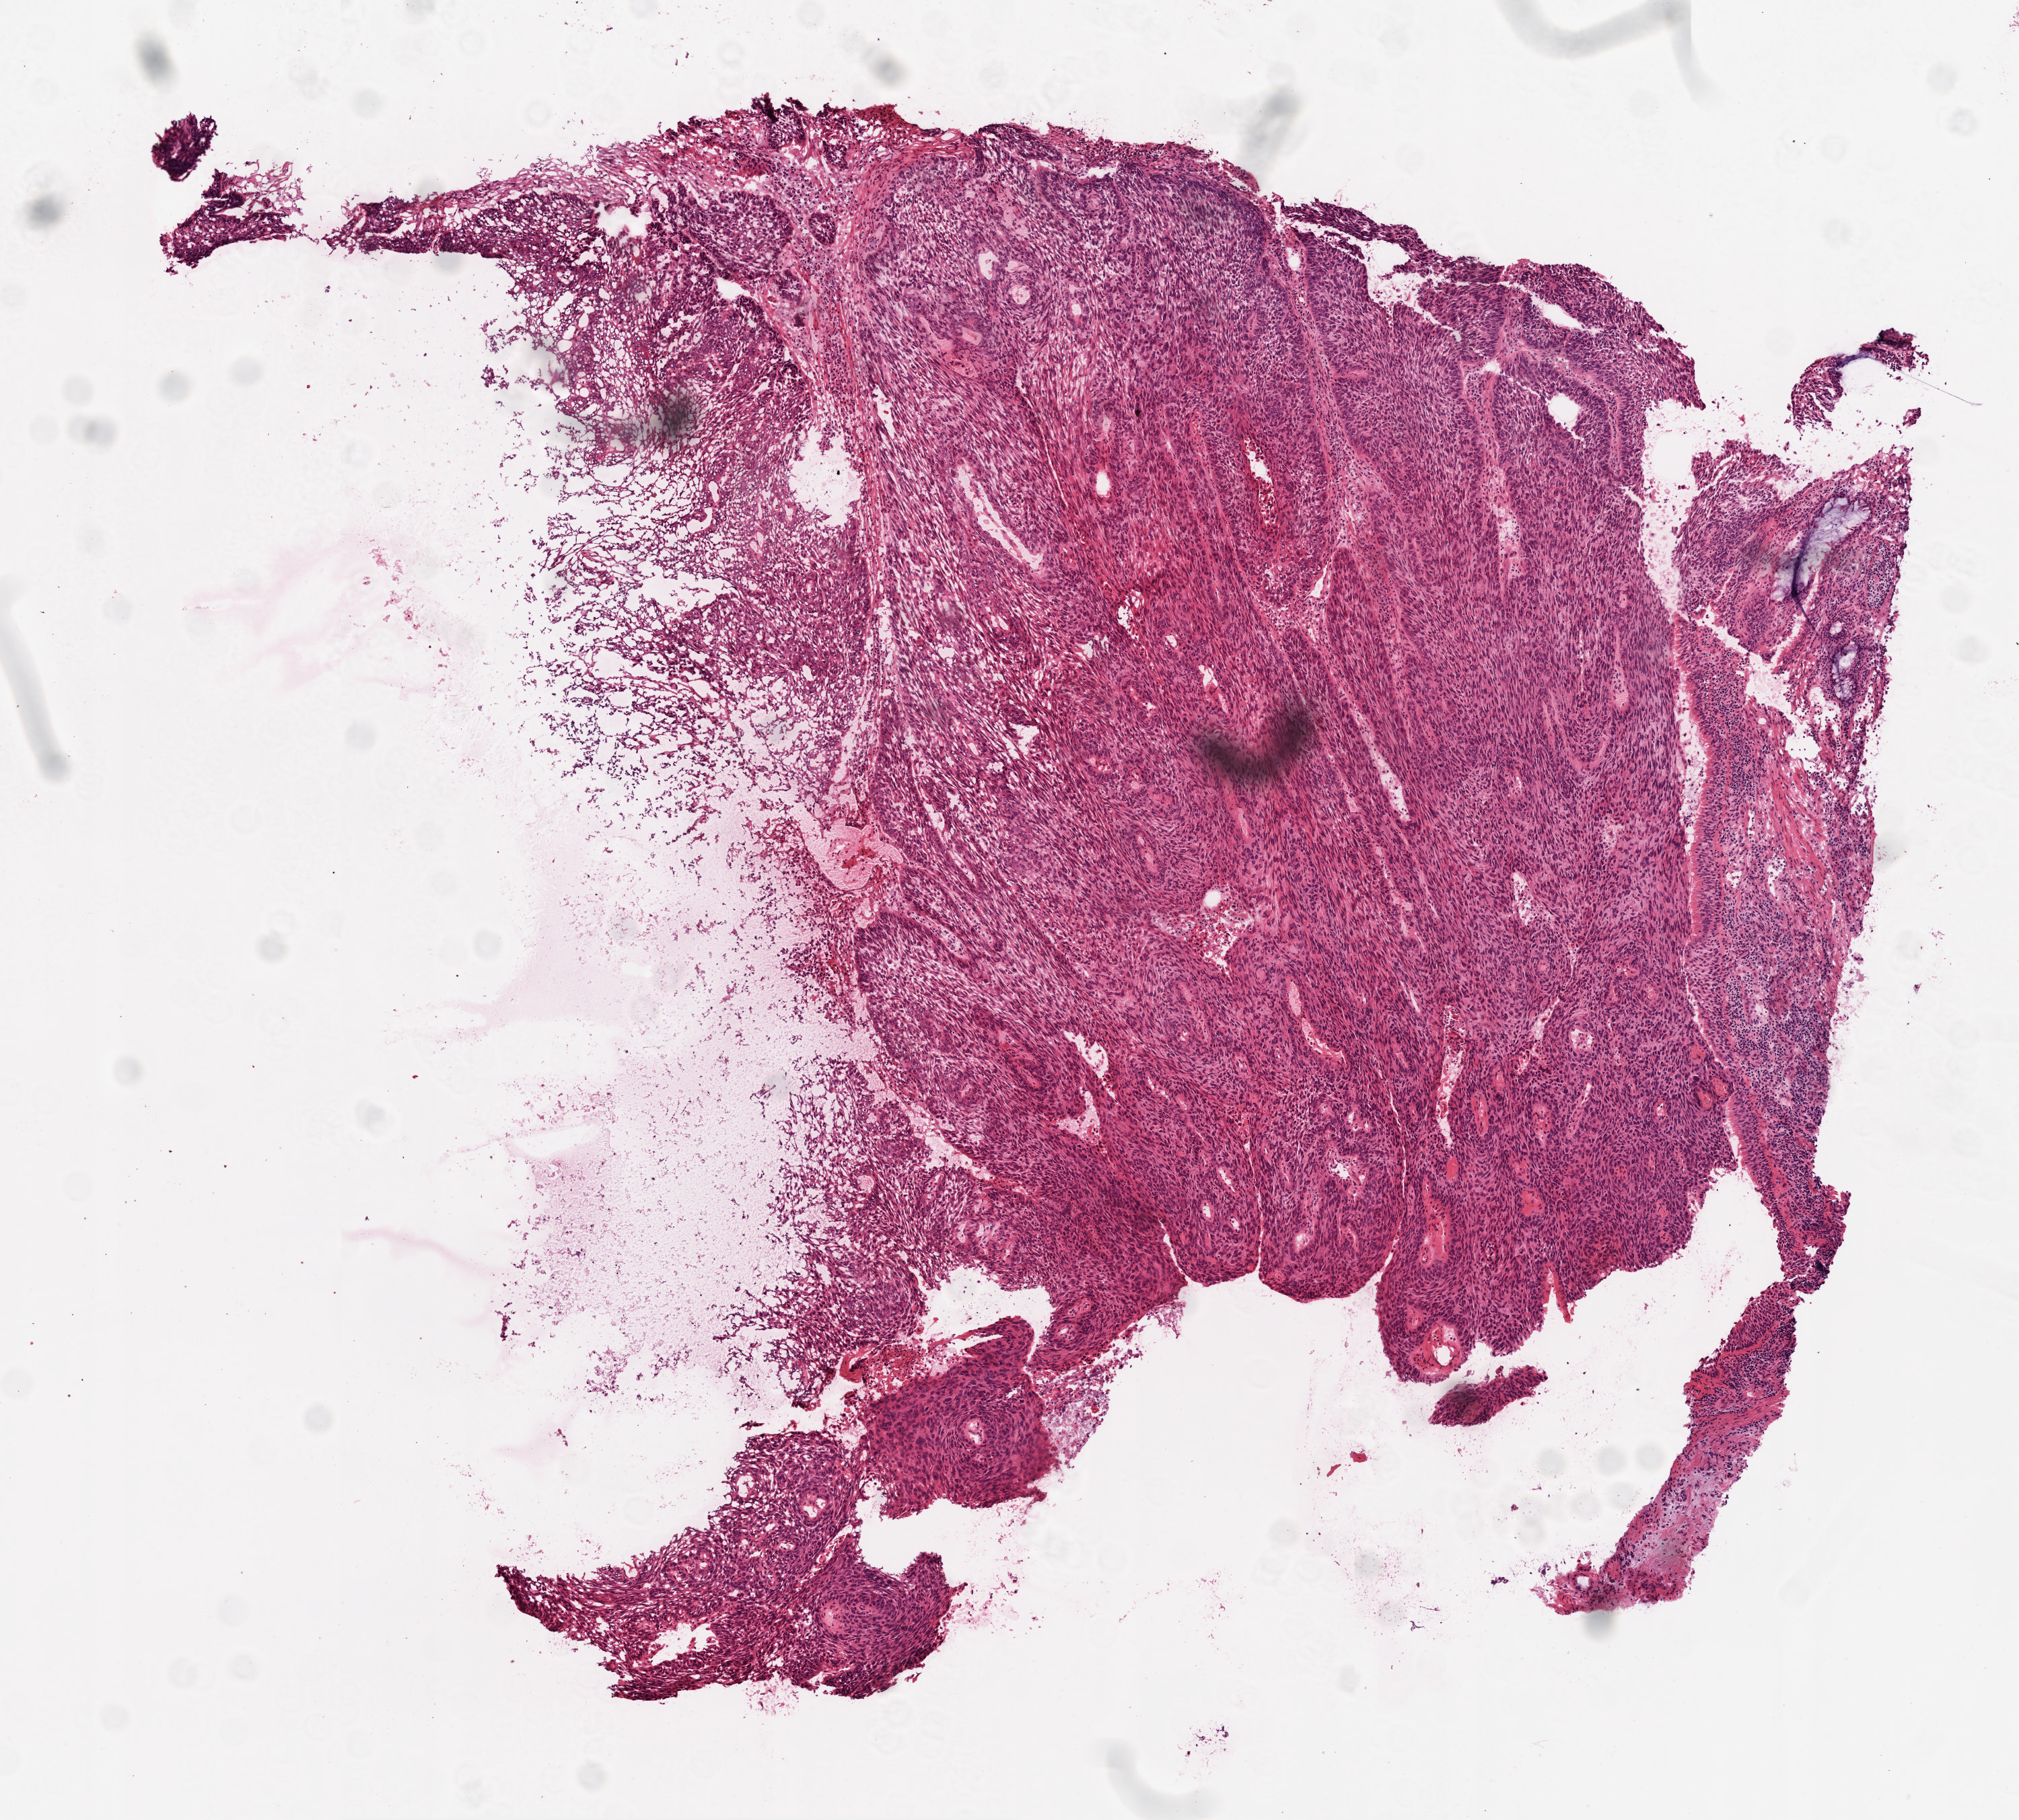
Digitized H&E tissue section (whole slide) — whole scanned area (about 6.0 x 5.4 mm, slide scanned at 20x) shown as a low-resolution overview. Frozen section from the top of the tissue portion. Lung, primary tumour sample. Male patient; age at initial diagnosis 66 years. Slide review estimates, as recorded: tumour cells 75%, tumour nuclei 70%, normal cells 15%, stromal cells 10%, necrosis 0%.
TNM: T2 N2 M0. Diagnosis: Squamous cell carcinoma, NOS (upper lobe, lung). AJCC pathologic stage: IIIA (6th edition). Laterality: left.